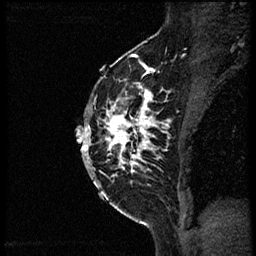
Breast MRI (dynamic contrast-enhanced), one sagittal slice. Dynamic contrast-enhanced study with each time point stored as its own series, time point 2 of 3 at this slice position (early post-contrast, ordered by acquisition time). 1.5 T. TE 4.2 ms, TR 21.3 ms. 2 mm slice thickness. 256 × 256 image matrix. Patient: female, 41 years. From the clinical record (not read from this slice): setting: breast cancer imaged before/during neoadjuvant chemotherapy; receptor status: HER2-positive.
Structures marked on this image (semi-automatically segmented with operator editing):
- analysis volume of interest (the breast-tissue region the enhancement analysis was run in; not a lesion): bounding box (x1, y1, x2, y2) in pixels: (88, 73, 170, 205)
- tumour enhancement mask (voxels above the 100 % enhancement threshold inside the analysis volume of interest): (88, 84, 167, 185)